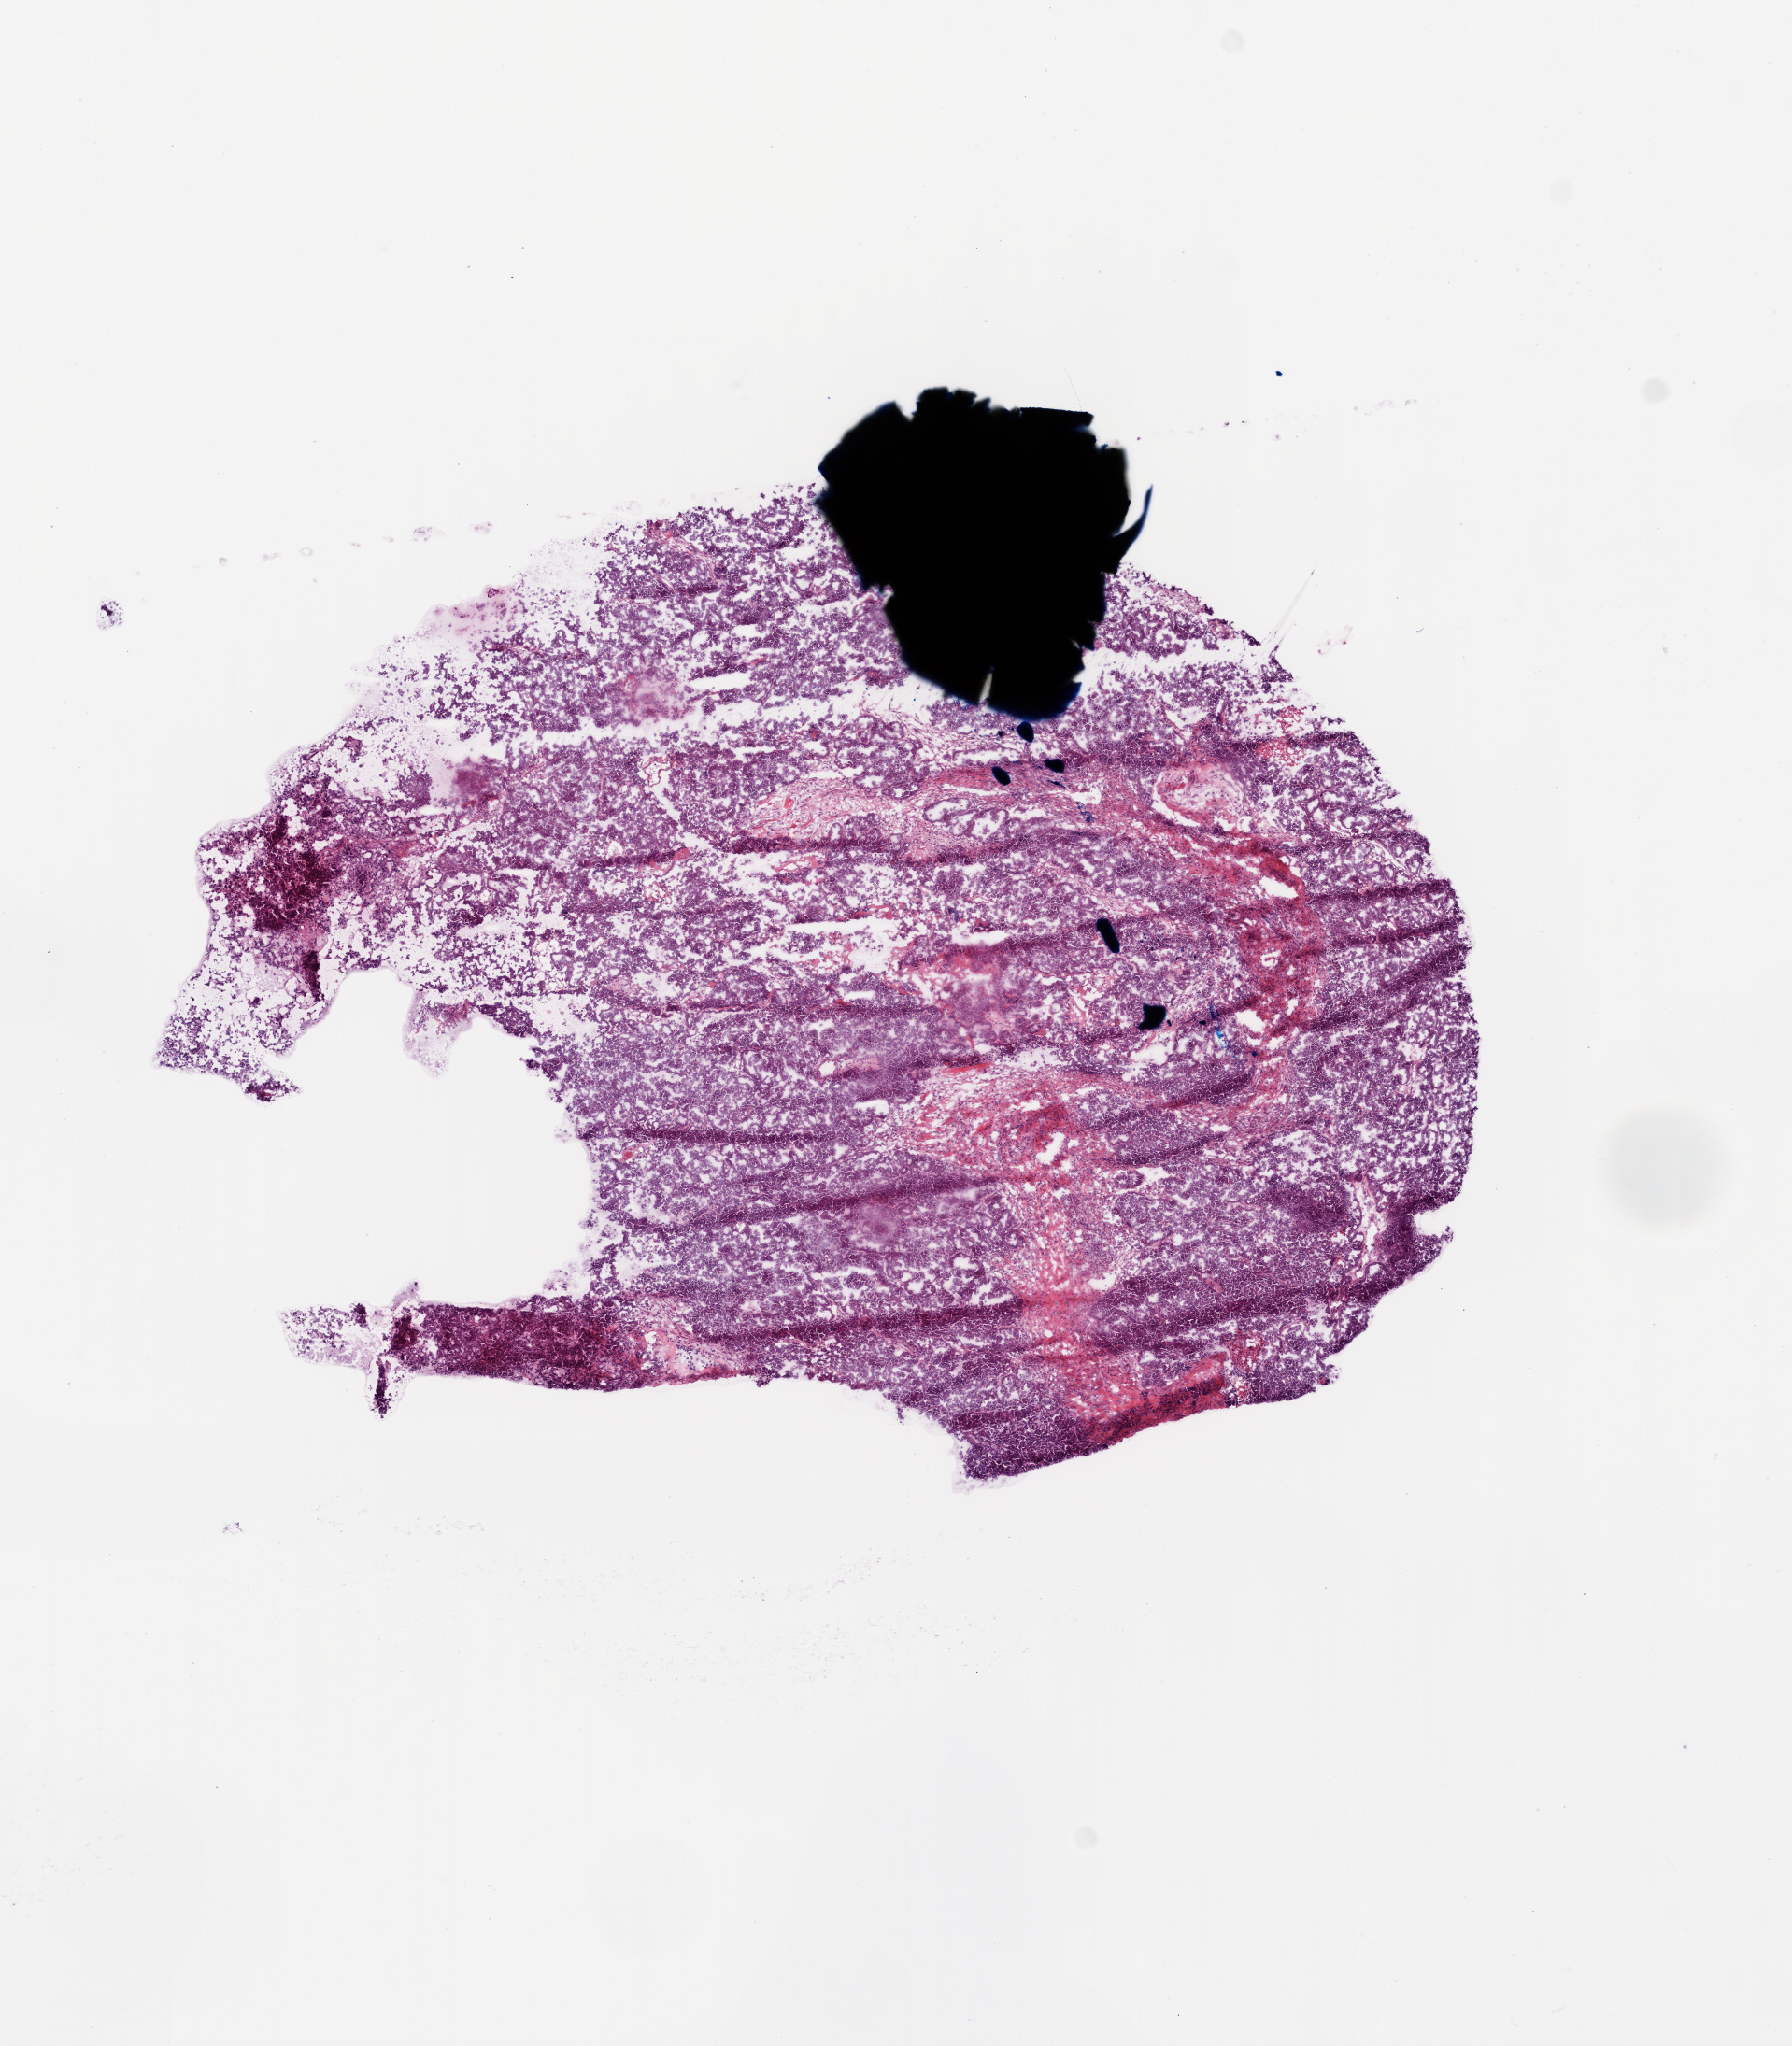
H&E whole-slide image, low-resolution overview of the scanned area, about 7.7 x 8.8 mm (from a 20x scan); frozen section; primary tumour sample from the ovary. Patient: female, age at initial diagnosis 68 years. Histologic grade: G3 (poorly differentiated). Pathologist review of this section (percent, as recorded): tumour cells 85%, tumour nuclei 85%, normal cells 5%, stromal cells 10%, necrosis 0%.
Laterality: bilateral. FIGO stage: IIIC. Diagnosis: Serous cystadenocarcinoma, NOS.